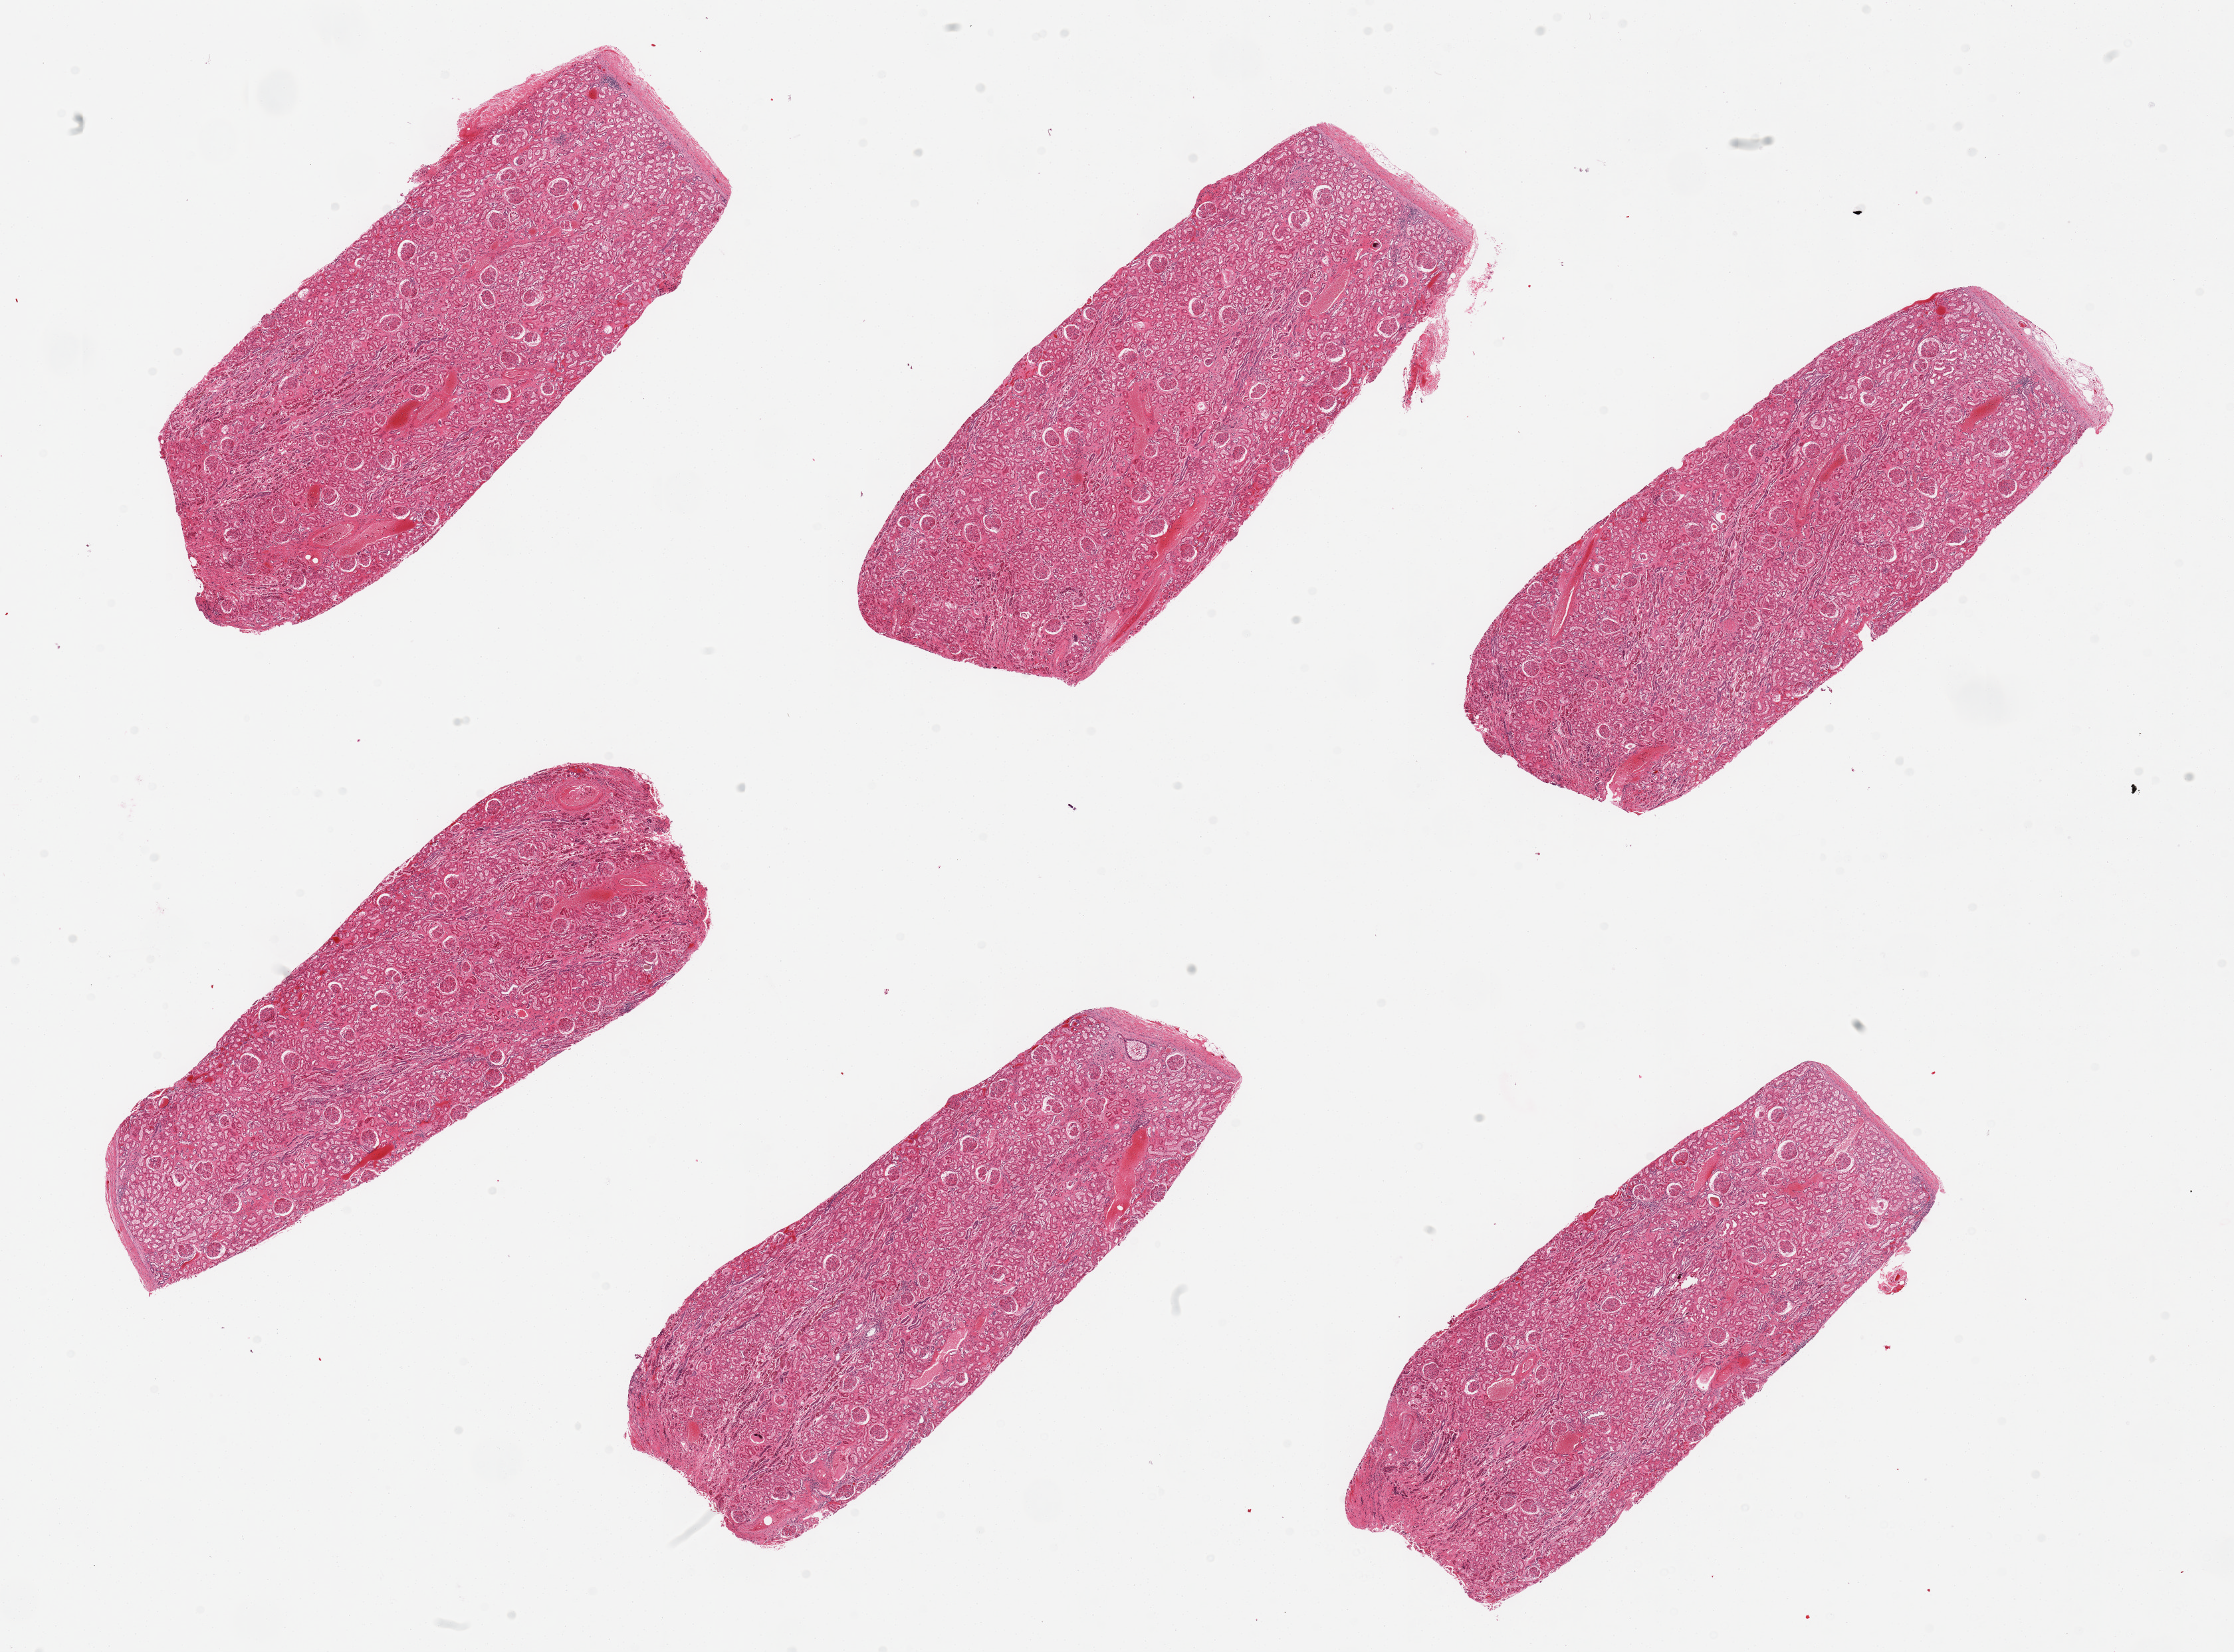
H&E whole-slide image — shown as a low-resolution overview of the whole scanned area (about 26.6 x 19.7 mm, slide scanned at 20x). PAXgene-fixed, paraffin-embedded tissue. Target tissue: renal cortex. Donor tissue sample. Donor: male.
• pathologist's review note for this sample: 6 pieces; vascular congestion; no glomerular lesions